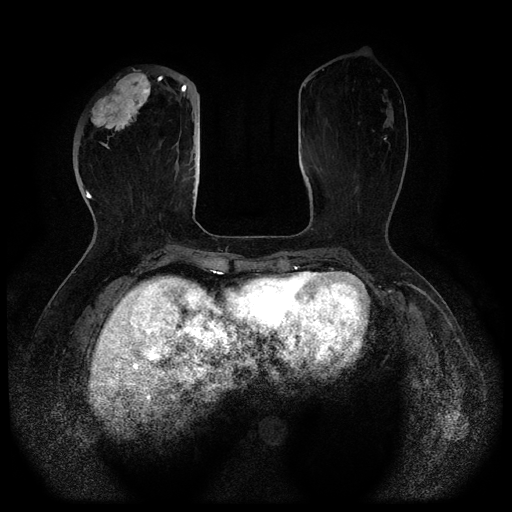
Breast MRI (dynamic contrast-enhanced, multi-phase), one axial slice. Position 33 of 116 along the scan axis. Dynamic contrast-enhanced series, time point 2 of 5 at this slice position (early post-contrast). 1.5 T. TE 2.6 ms, TR 5.3 ms. 2 mm slice thickness. 512 × 512 image matrix. Female patient, age 51 years.
Annotated regions visible in this slice (semi-automatically segmented with operator editing):
- breast lesion (labelled 'tumour' in the annotation; benign lesions carry a separate 'benign' label): box from (x=90, y=70) to (x=151, y=149) px